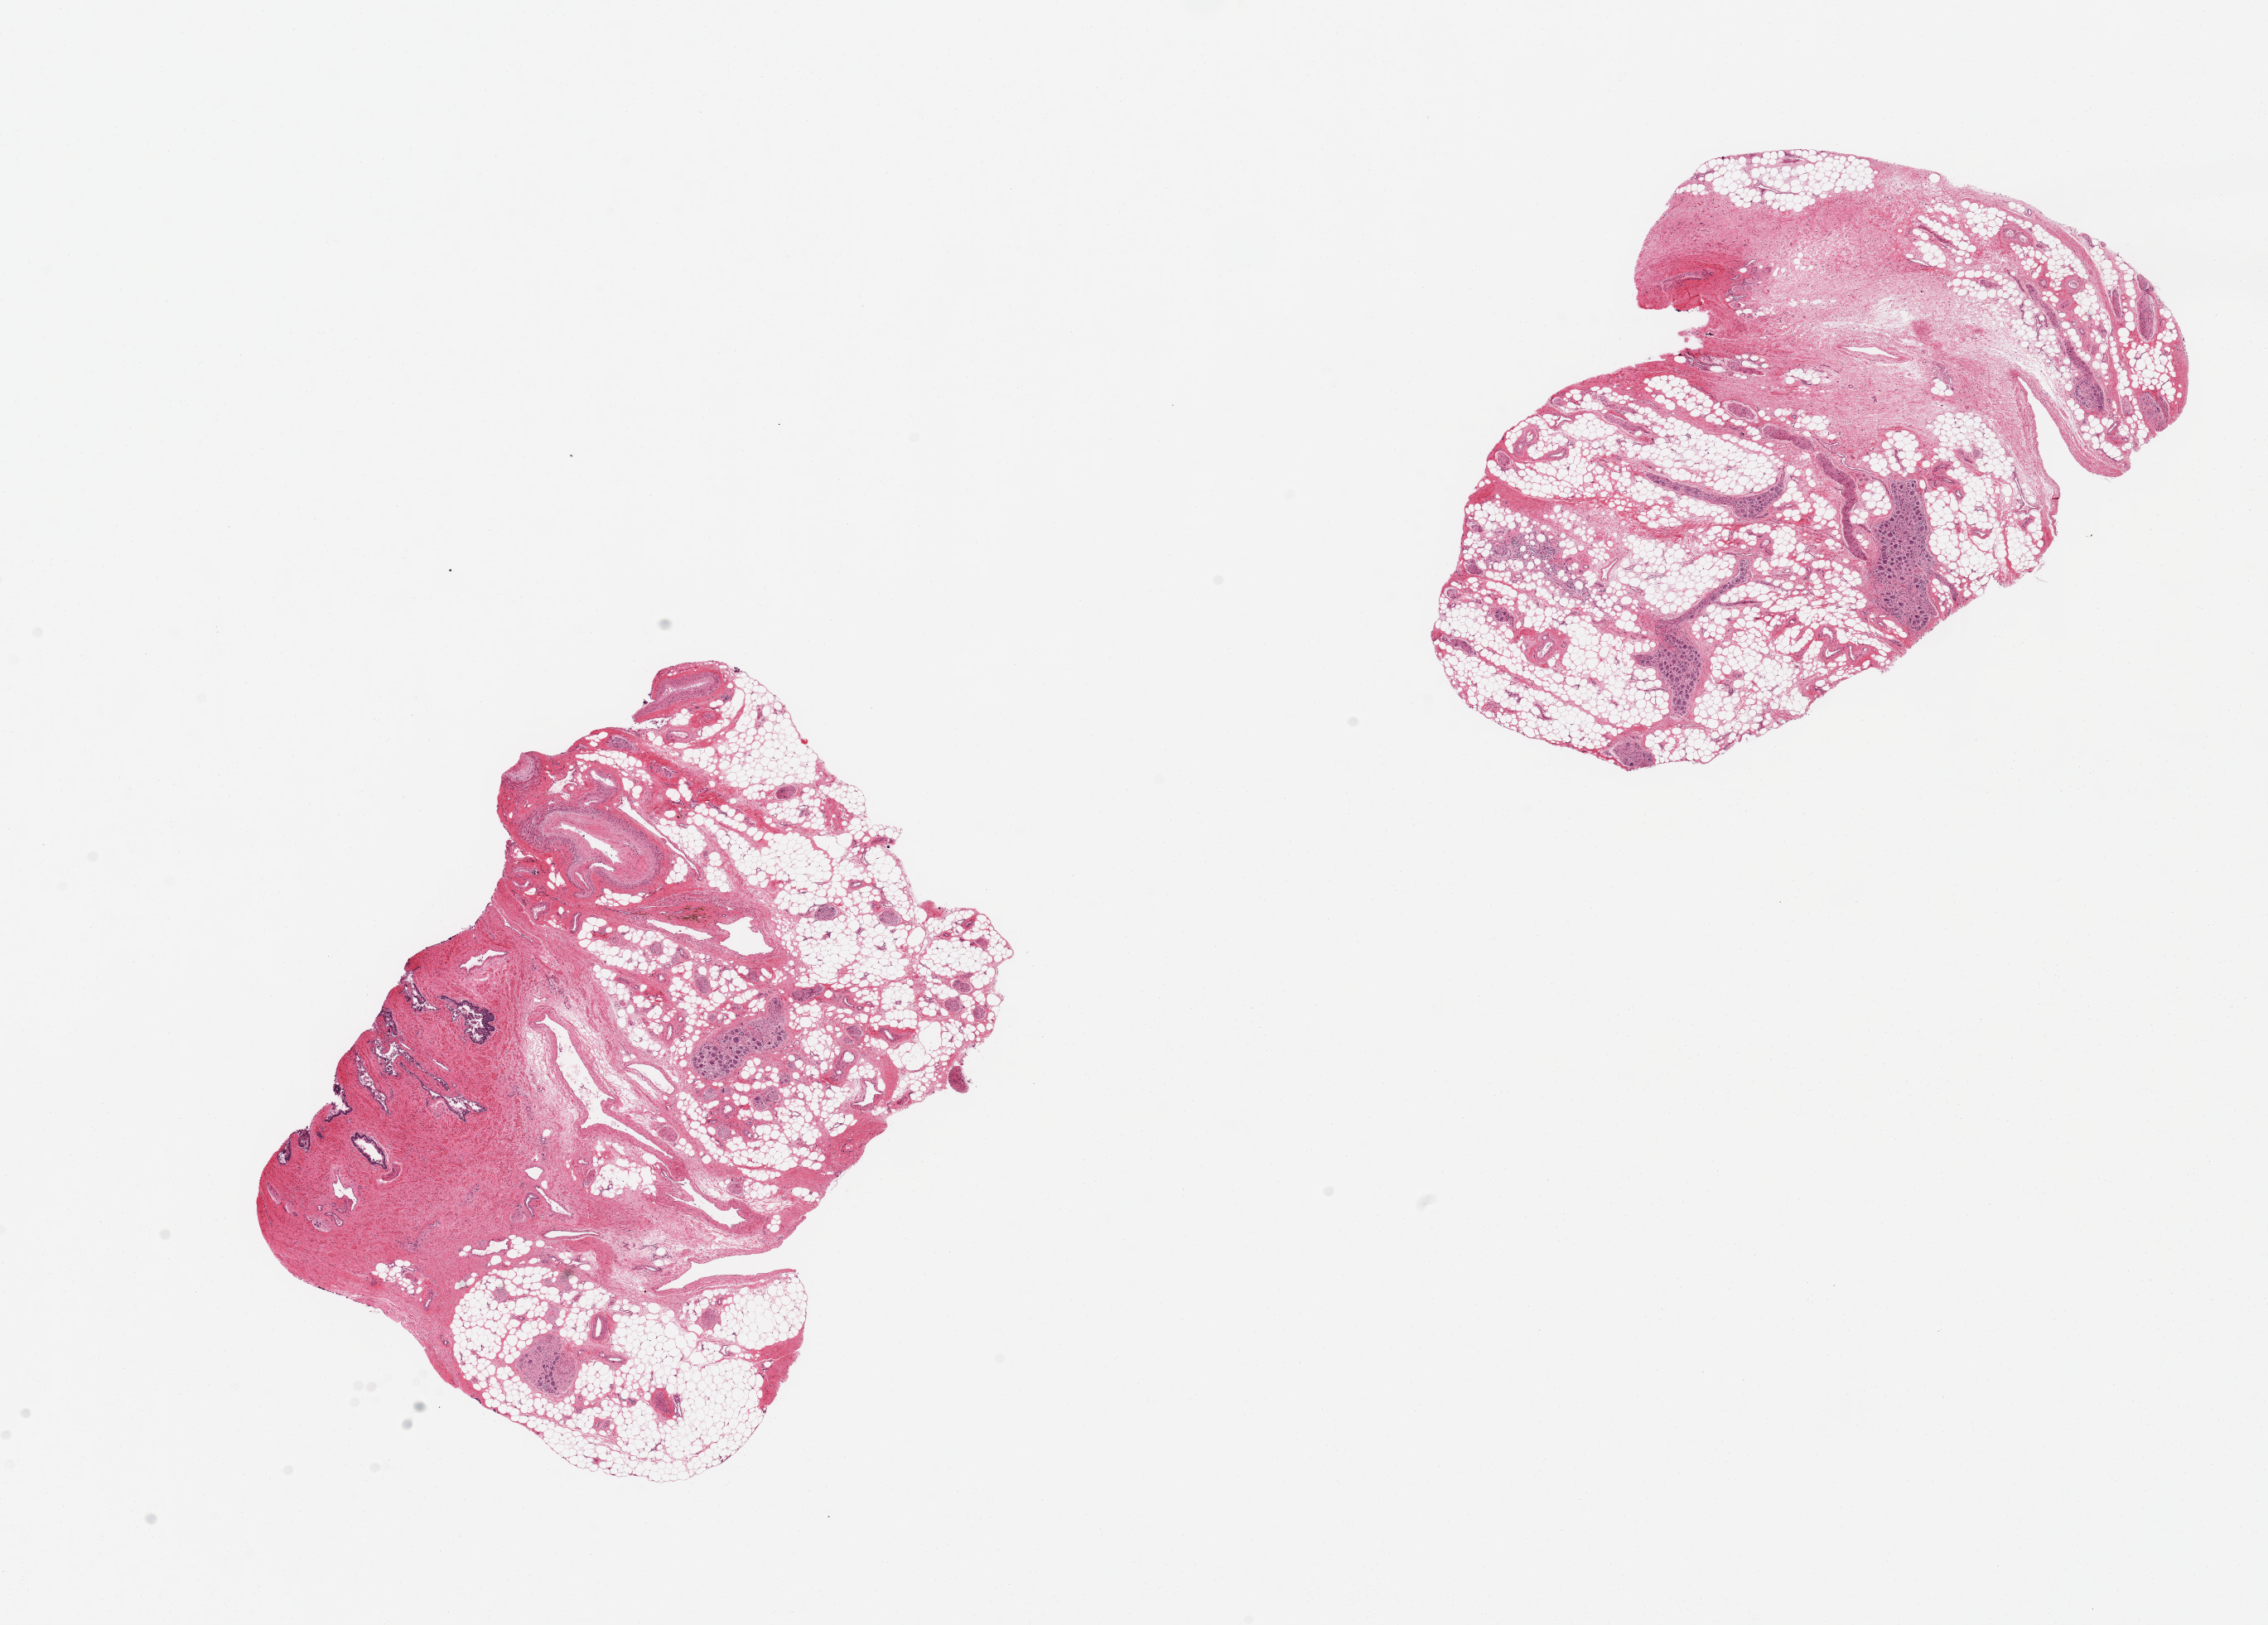
Whole-slide image, haematoxylin and eosin stain, low-resolution overview of the scanned area, about 21.7 x 15.5 mm. Donor sex: male.
Specimen: PAXgene-fixed paraffin-embedded (PFPE) section; section of prostate (target tissue); donor tissue sample.